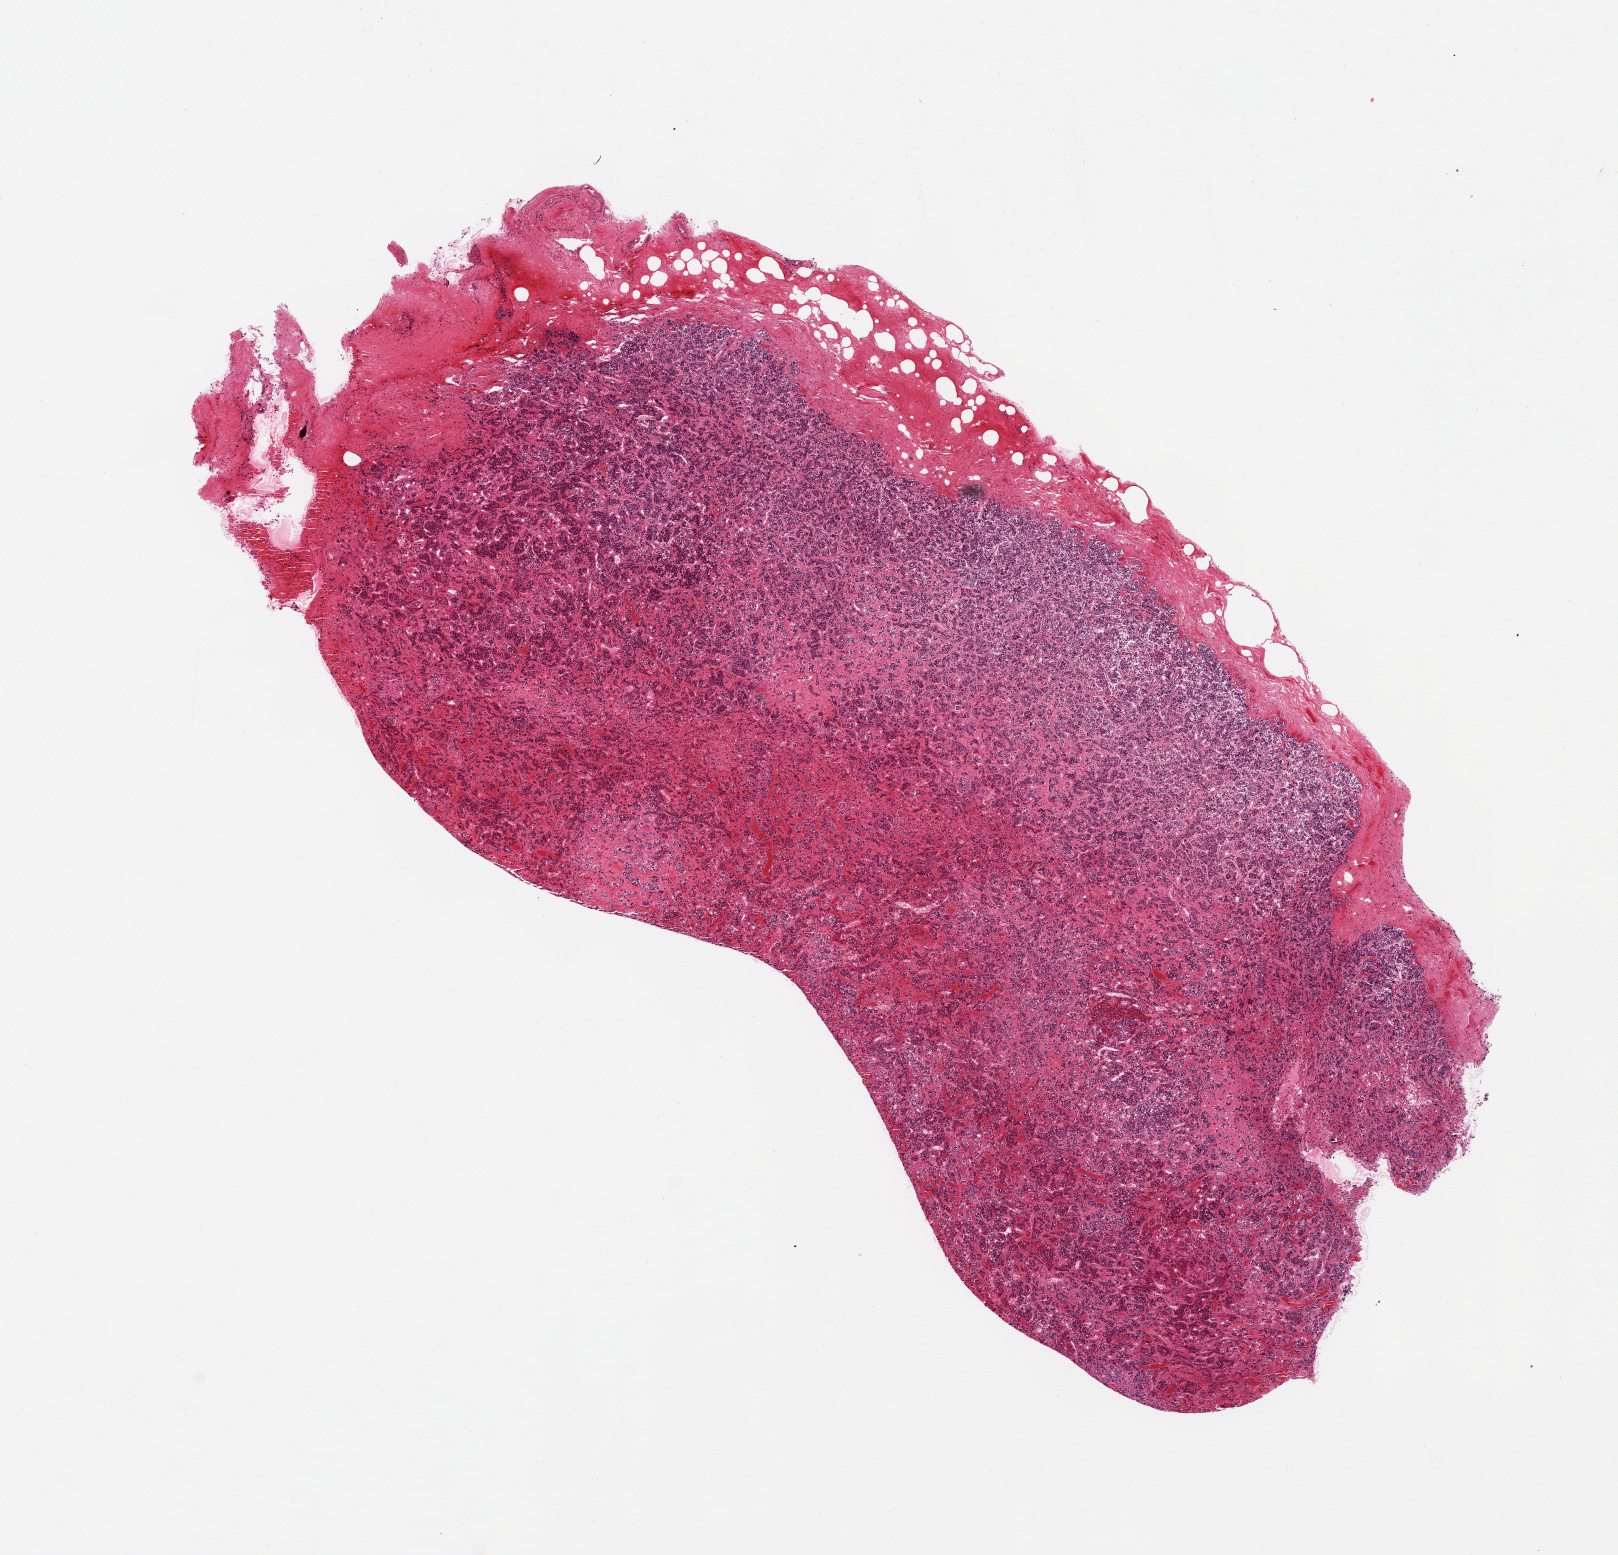
Digitized hematoxylin and eosin (H&E)-stained section — whole scanned area (about 12.8 x 12.3 mm, acquisition: 20x scan) shown as a low-resolution overview; PAXgene-fixed paraffin-embedded (PFPE) section; sampled site (target tissue): pituitary; donor tissue sample. Donor sex: male.
Reviewer comment on this tissue sample: 1 piece, adenohypophysis.